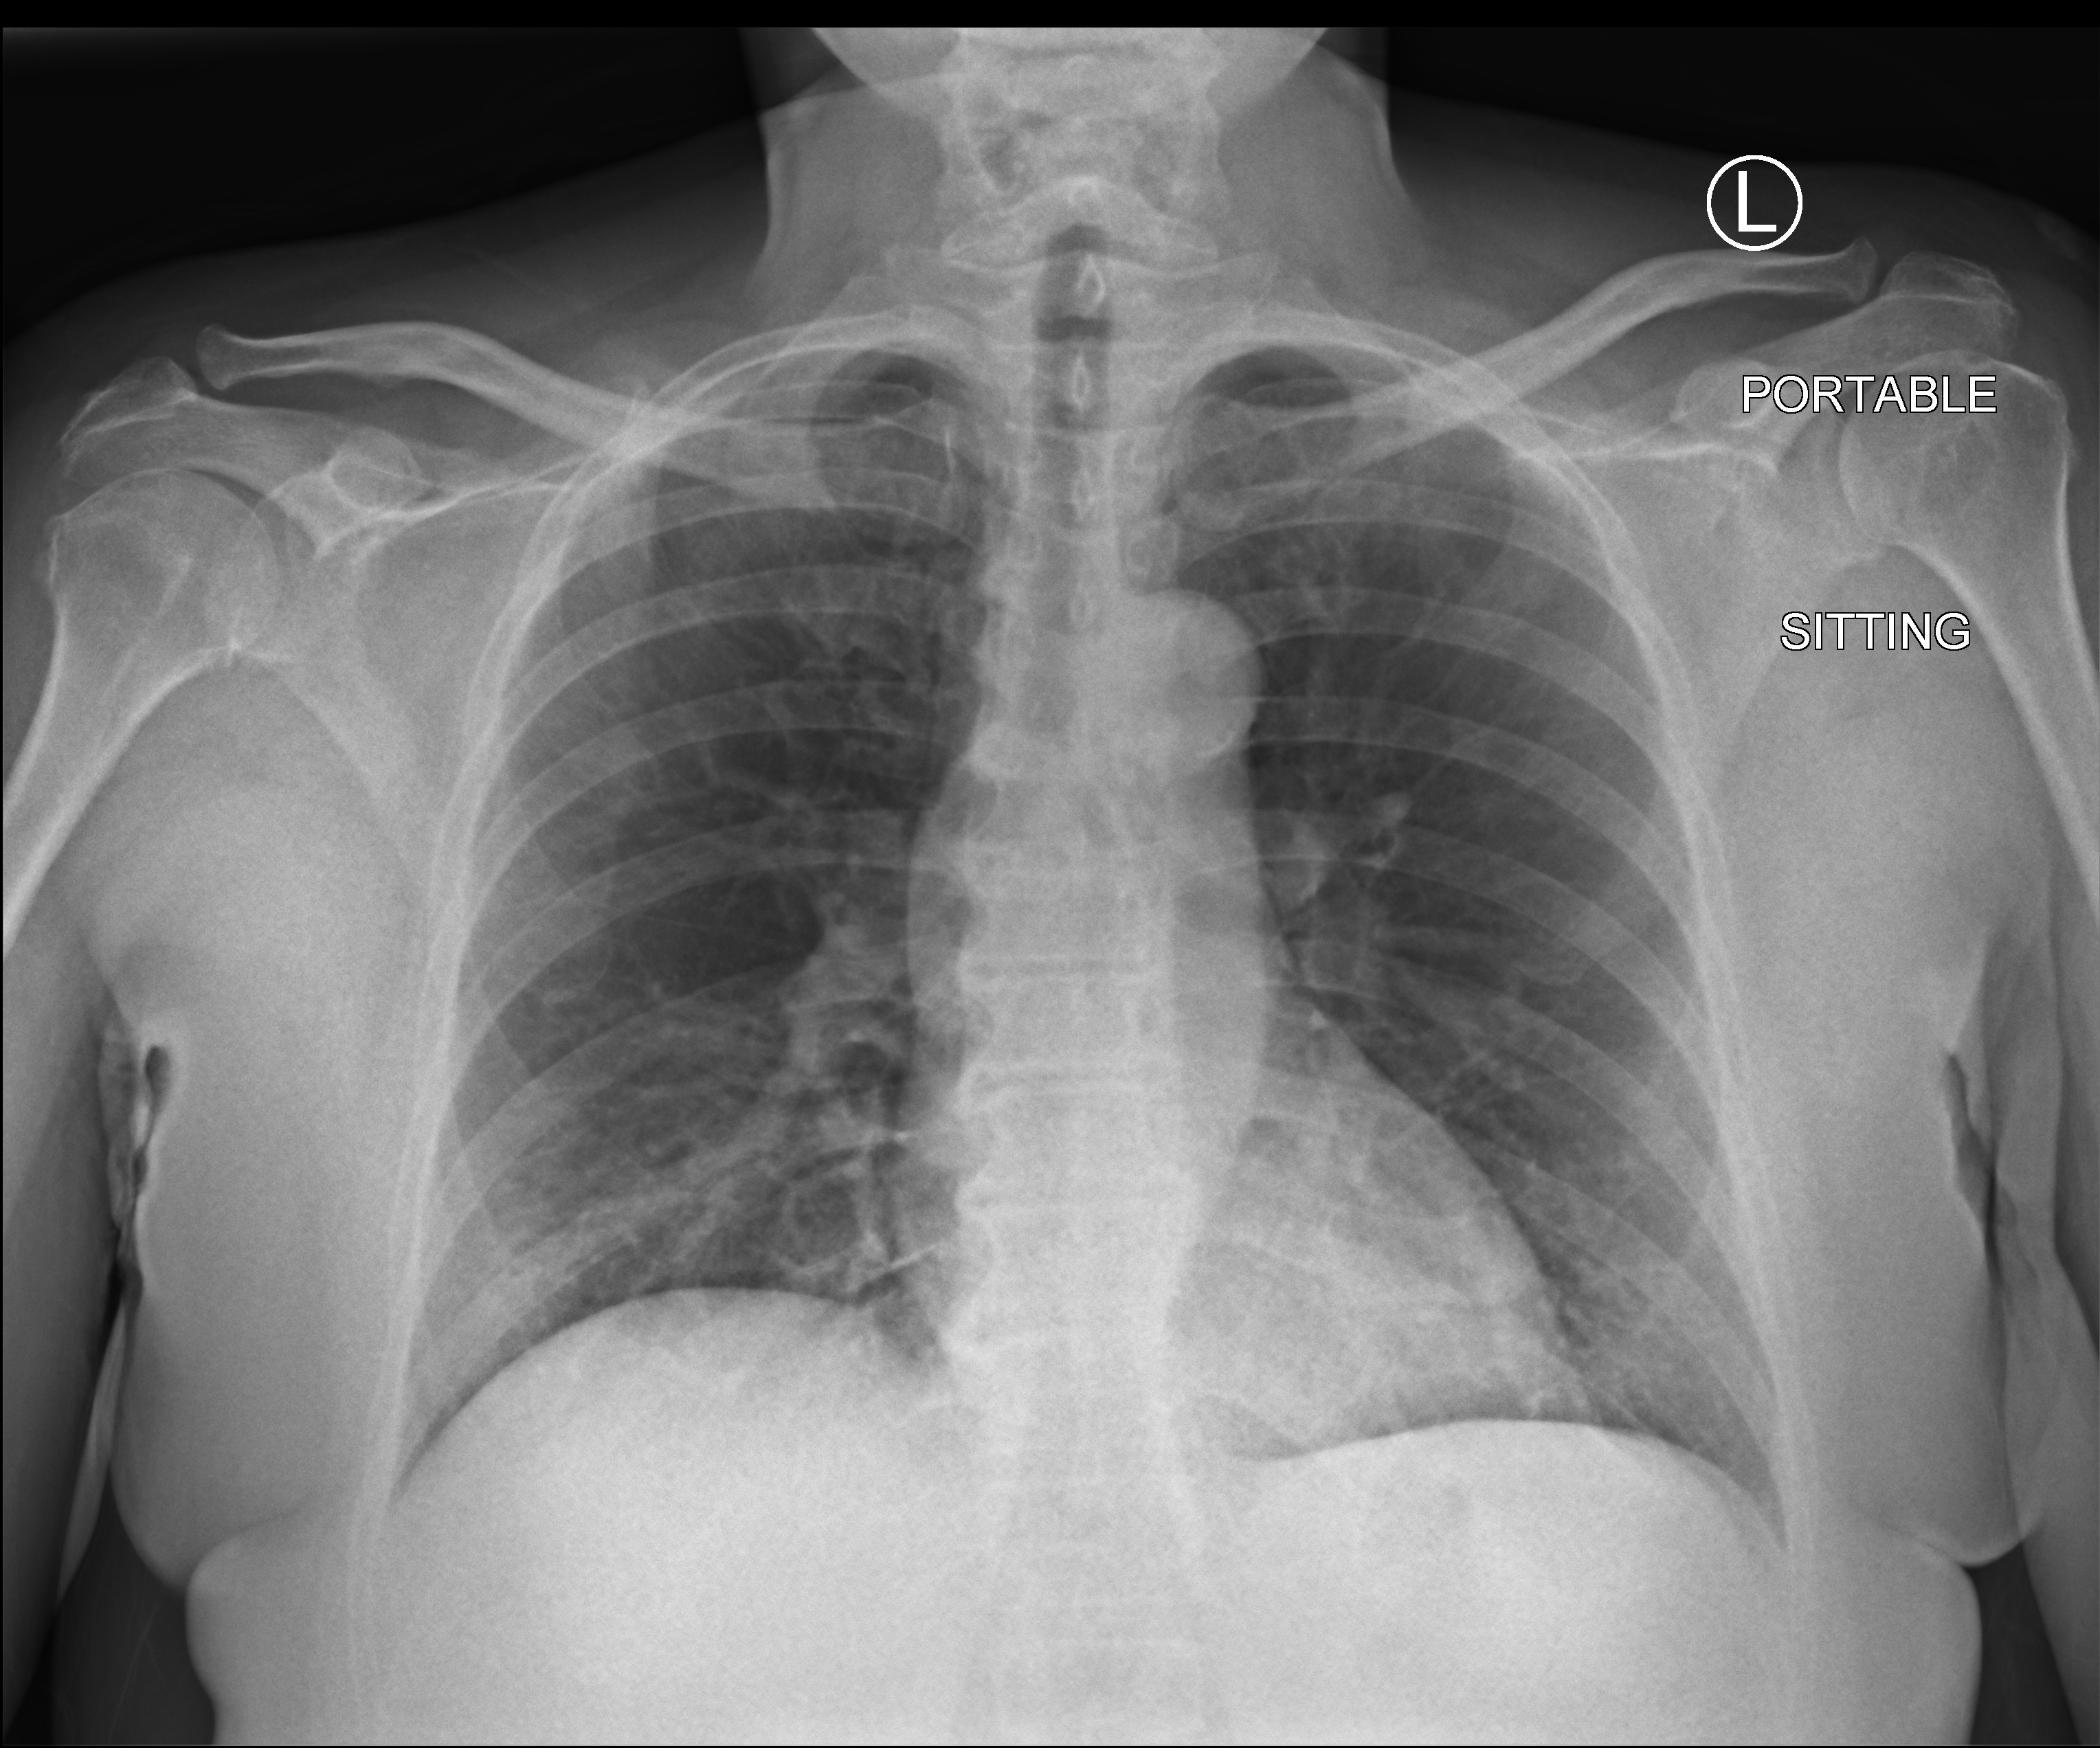
Portable chest radiograph; anteroposterior (AP) projection. Patient hospitalised with COVID-19; female, aged 18–59 years.
From the hospital-stay record, not from the radiograph (when in the stay this image was taken is not recorded):
- admitted to intensive care during this hospital stay: no
- other chronic lung disease (admission record): no